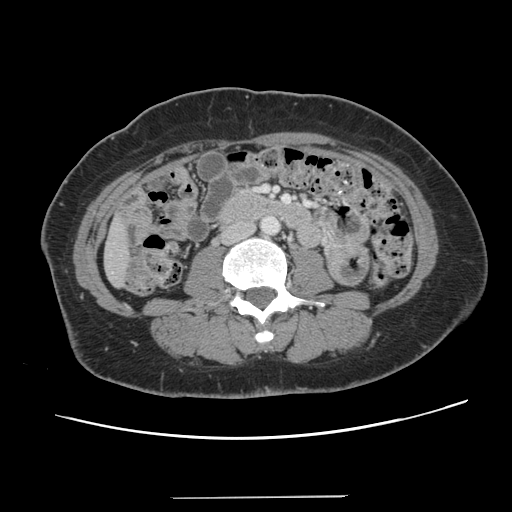
Contrast-enhanced abdominal CT, one axial slice; slice 22 of 141 in the series (ordered by position); 120 kVp; intravenous contrast given; soft-tissue window (W 400 / L 40 HU); 512 × 512 image matrix, field of view 366 × 366 mm. Female patient, age 53 years. Case-level facts recorded for this patient, not image findings: diagnosis: colorectal cancer liver metastases, imaged before liver resection.
Structures marked on this image (expert manual segmentation):
- liver: box from (x=105, y=221) to (x=130, y=286) px
- planned liver remnant (the part of the liver to remain after resection): (x=106, y=222)–(x=130, y=286)